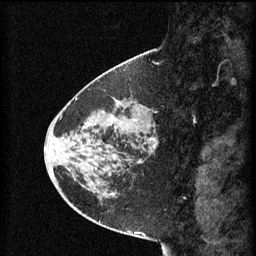
Breast MRI (dynamic contrast-enhanced), one sagittal slice; slice 24 of 60 in the series (ordered by position); 3 images stored at this slice position (order not interpretable as contrast timing); 1.5 T; TE 4.2 ms, TR 8.2 ms; 256 × 256 image matrix, field of view 200 × 200 mm. Female patient, age 45 years.
Annotated regions visible in this slice (semi-automatic segmentation, software-assisted and operator-edited):
- analysis volume of interest (the breast-tissue region the enhancement analysis was run in; not a lesion): bounding box (x1, y1, x2, y2) in pixels: (80, 102, 157, 171)
- tumour enhancement mask (voxels above the 70 % enhancement threshold inside the analysis volume of interest): (113, 118, 155, 163)